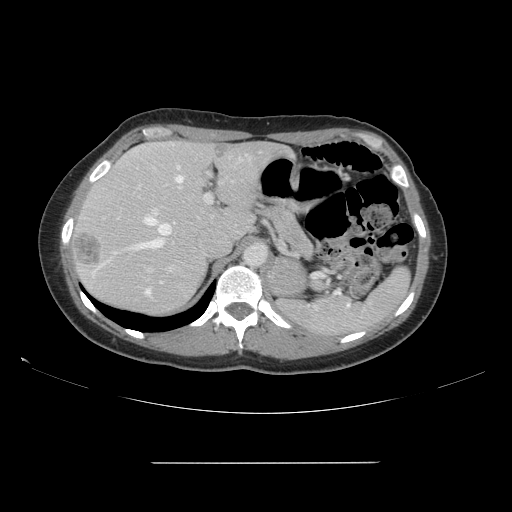
Contrast-enhanced abdominal CT, one axial slice. Slice 109 of 151 in the series (ordered by position). 120 kVp. Intravenous contrast given. Soft-tissue window (W 400 / L 40 HU). 2.5 mm slice thickness. 512 × 512 image matrix. Female patient, age 46 years. From the clinical record (not read from this slice): diagnosis: colorectal cancer liver metastases, imaged before liver resection; multiple liver metastases: yes; largest metastasis: 3 cm; disease in both lobes: yes.
Structures marked on this image (expert manual segmentation):
- hepatic veins: bounding box <92,154,251,274> (left, top, right, bottom; pixels)
- liver: <70,141,284,316>
- planned liver remnant (the part of the liver to remain after resection): <88,141,286,252>
- portal vein (with intrahepatic branches): <138,185,212,295>
- liver metastasis: <73,230,103,268>
- liver metastasis: <216,145,229,157>